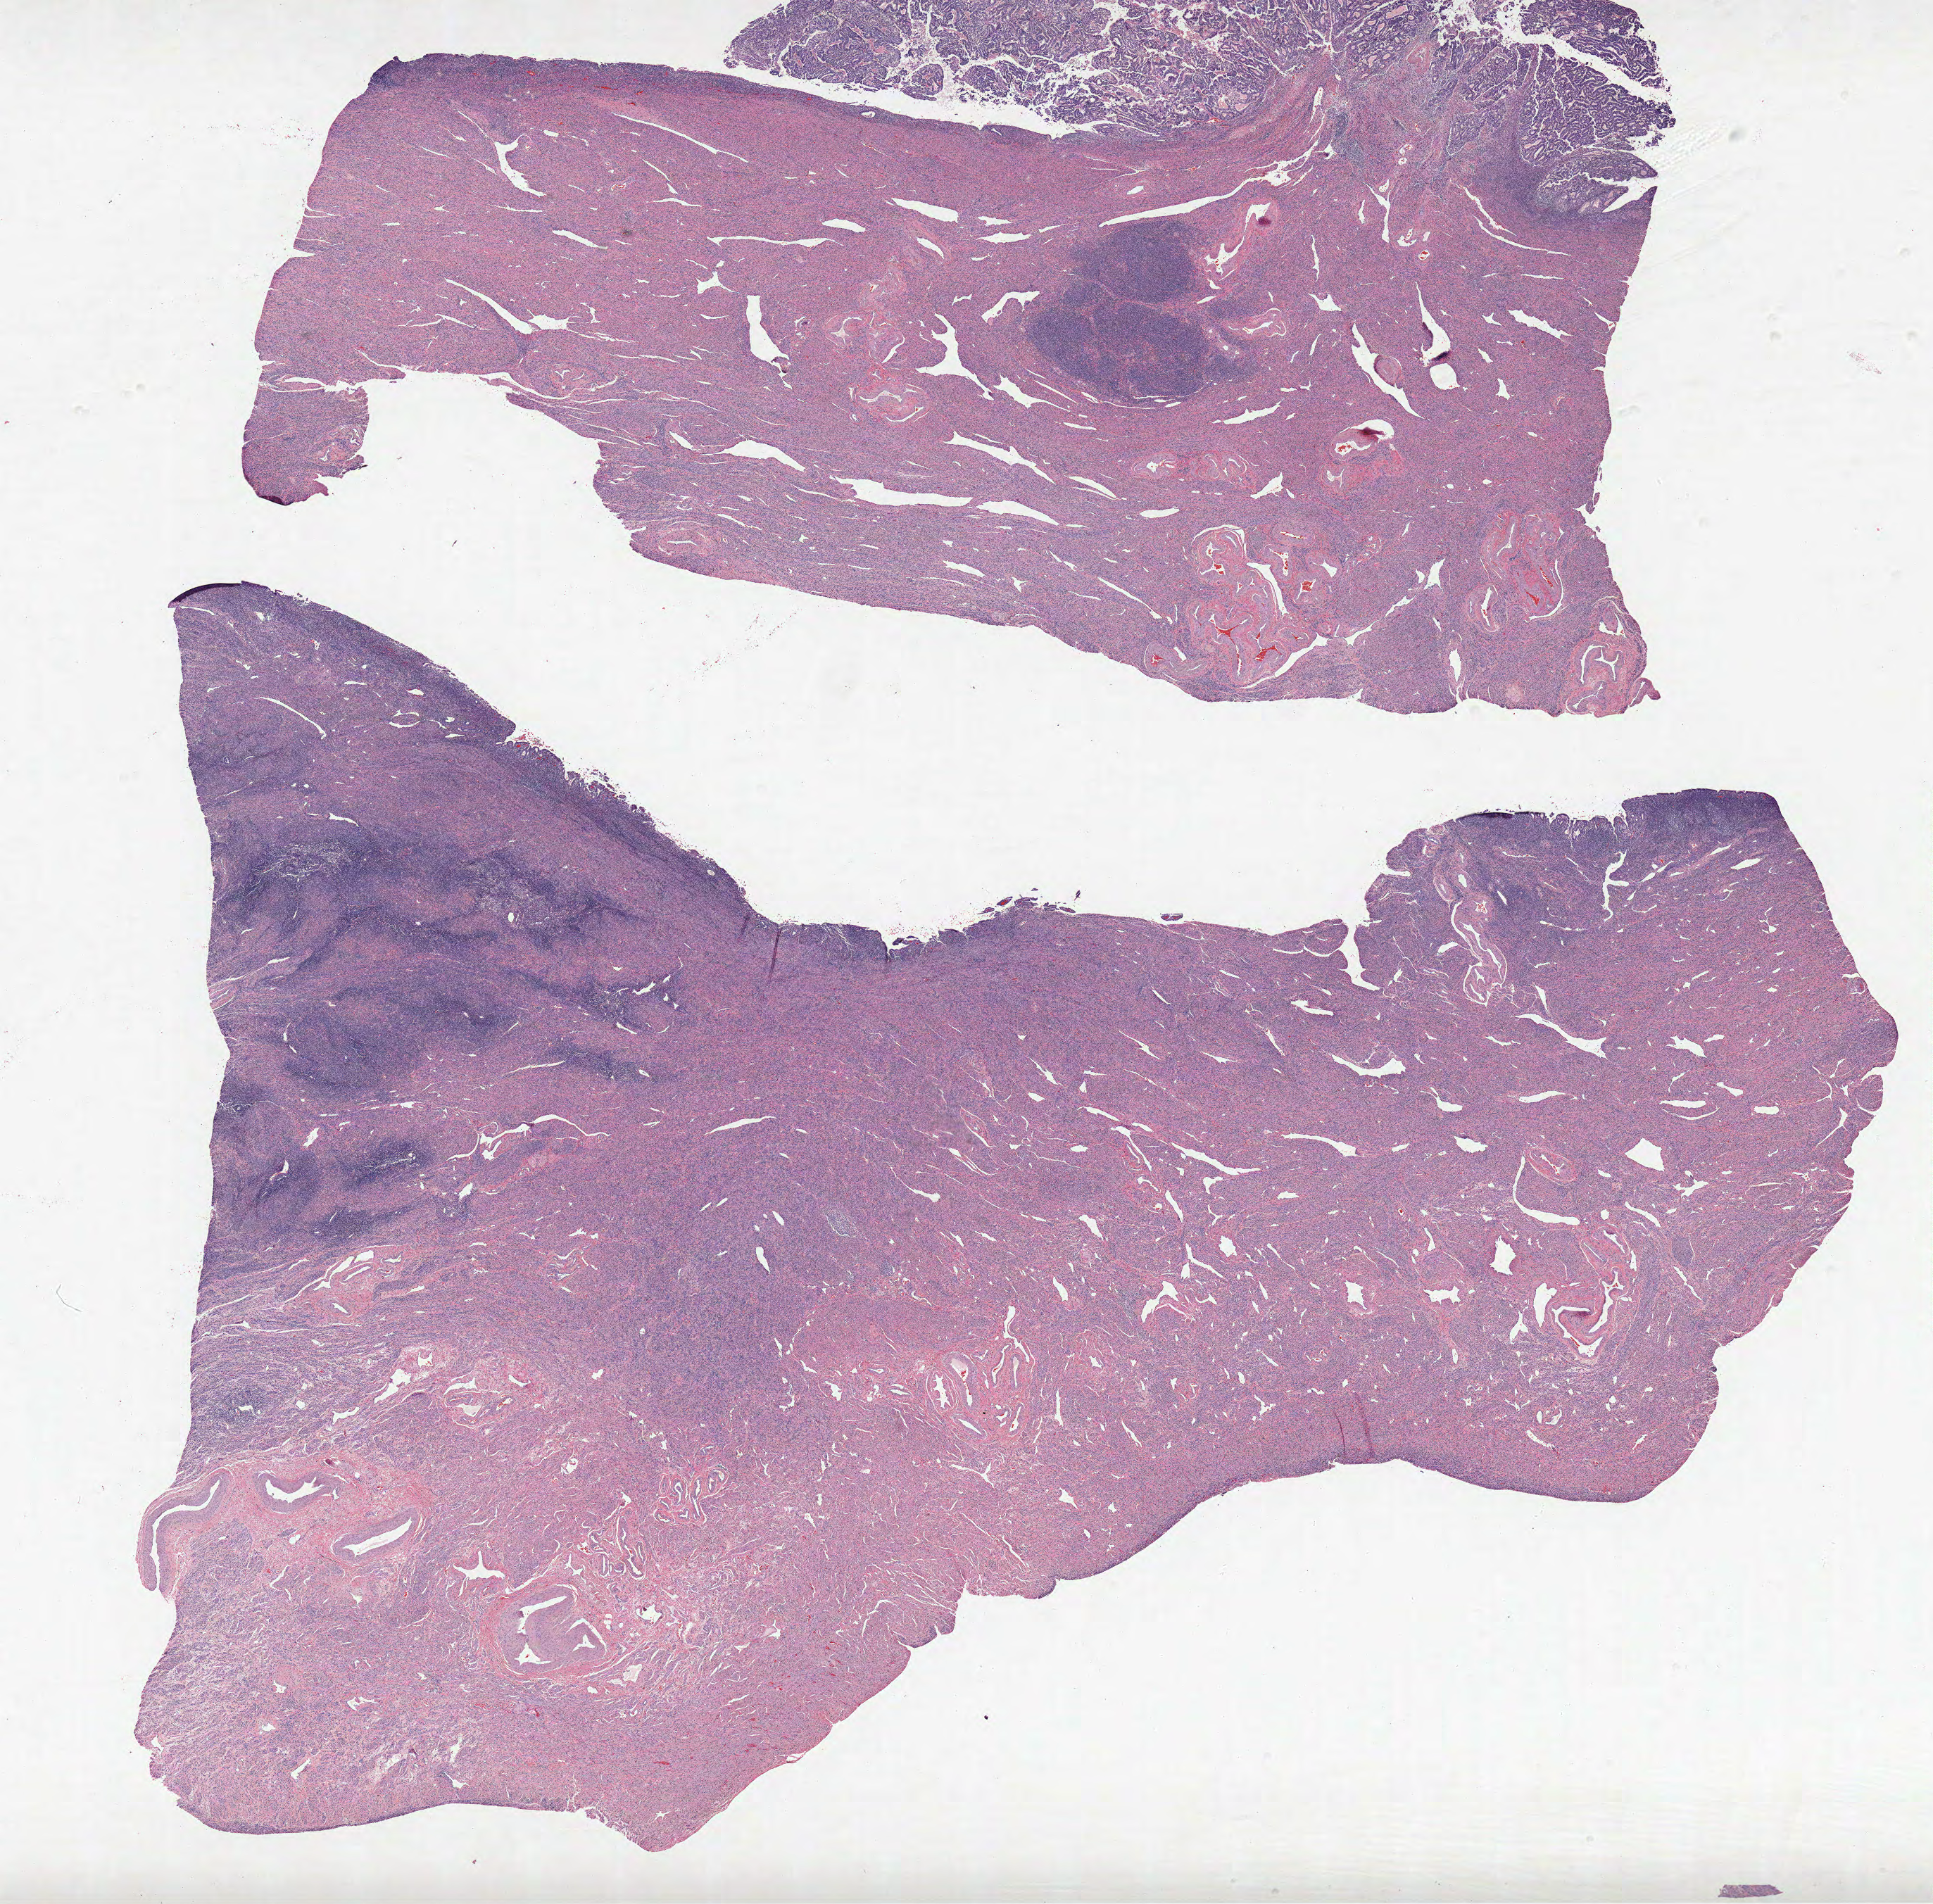
Whole-slide histology image, Hematoxylin and eosin (H&E) stained, shown as a low-resolution overview of the whole scanned area (about 21.9 x 21.6 mm, from a 20x scan), formalin-fixed paraffin-embedded (FFPE) diagnostic section, sample: primary tumour, uterus. Female, age 62 years at initial diagnosis. Histologic grade: G2 (moderately differentiated).
- histologic diagnosis: Endometrioid adenocarcinoma, NOS (endometrium)
- FIGO stage: IA